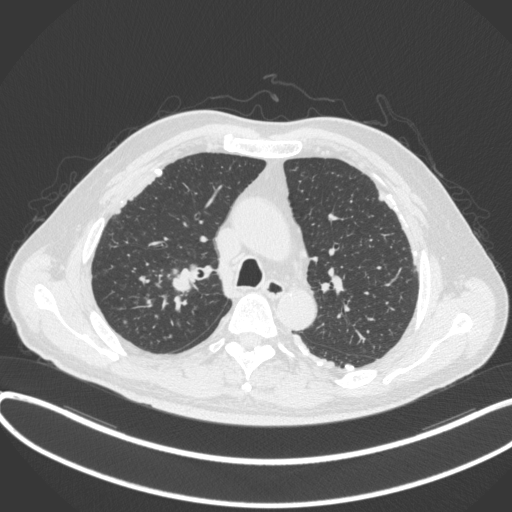
Chest CT, one axial slice; slice 294 of 455 in the series (ordered by position); reconstruction kernel B31f; lung window (W 1500 / L -600 HU); 512 × 512 image matrix, field of view 400 × 400 mm. Patient: male, 58 years. Case-level facts recorded for this patient, not image findings: clinical TNM (as recorded): T1c N0 M0.
Outlined on this slice (bounding box drawn by a radiologist):
- lung tumour (recorded histology: squamous cell carcinoma): bounding box (x1, y1, x2, y2) in pixels: (170, 264, 201, 296)